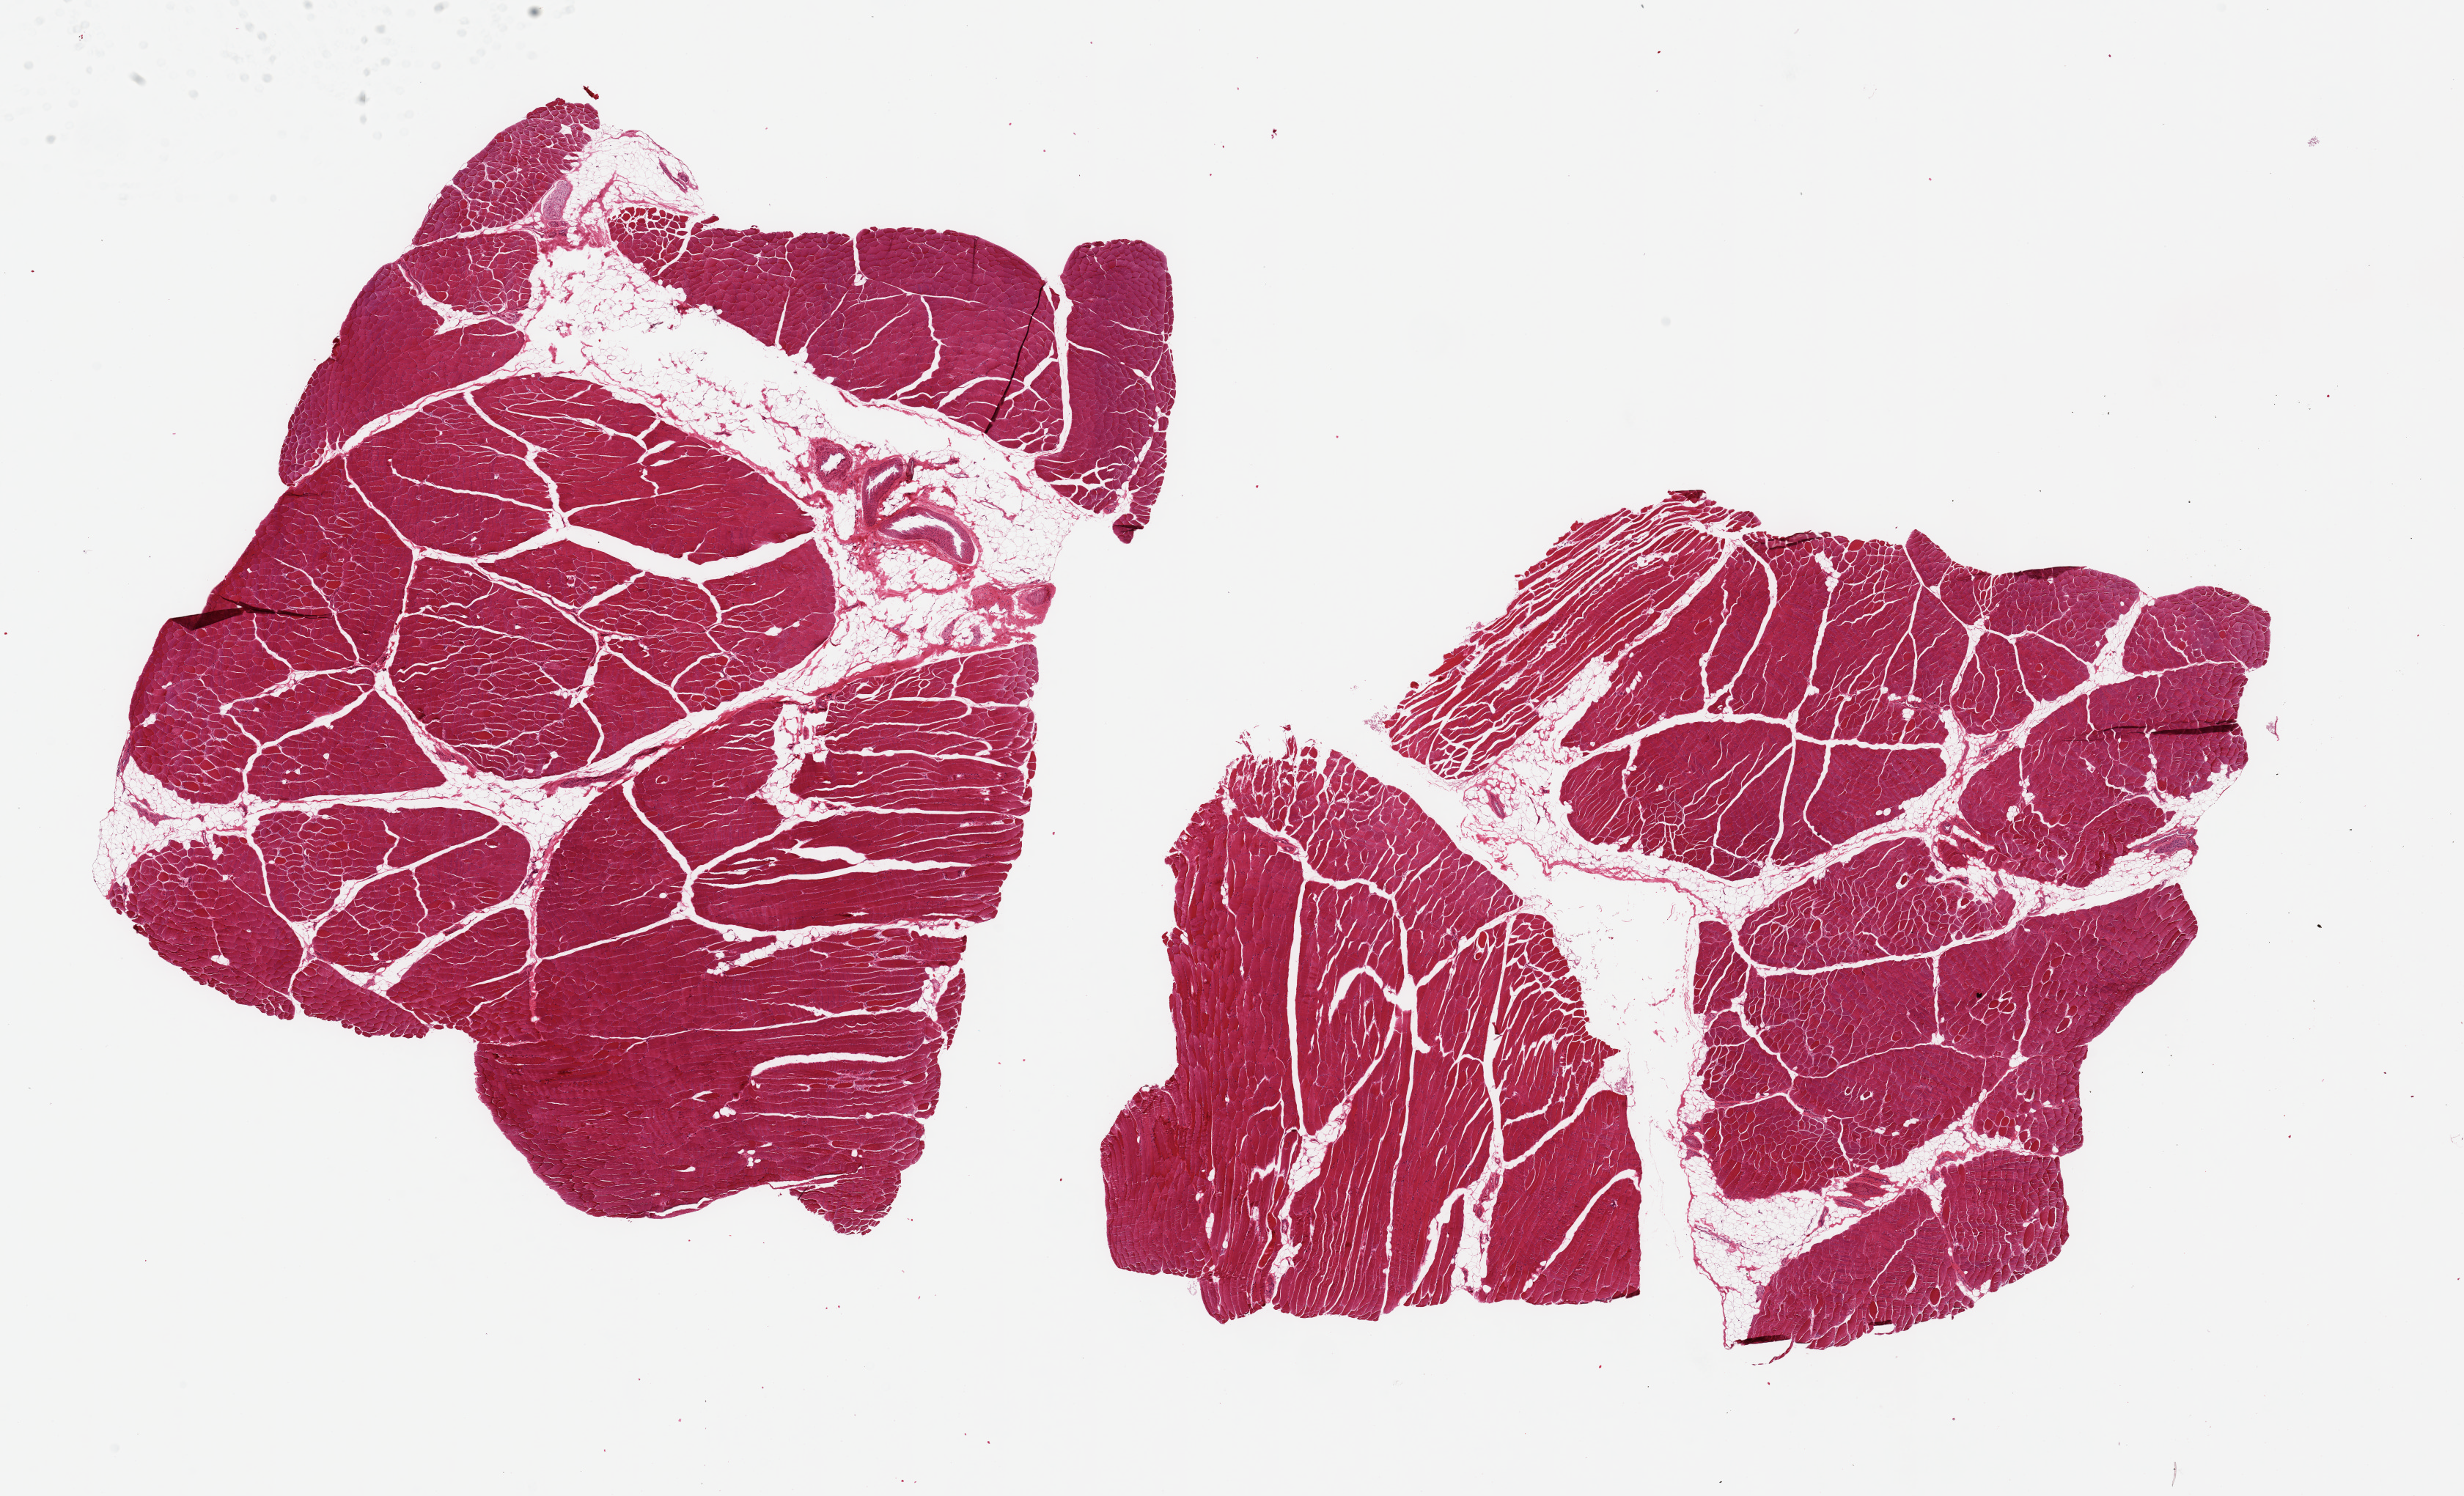
Digitized haematoxylin and eosin-stained section — shown as a low-resolution overview of the whole scanned area (about 26.6 x 16.1 mm, acquisition: 20x scan); PAXgene-fixed, paraffin-embedded tissue; target tissue: skeletal muscle; donor tissue sample. Donor: female.
Review note (as recorded): 2 pieces, 12x9 & 12x10mm; ~20% interstital fat.